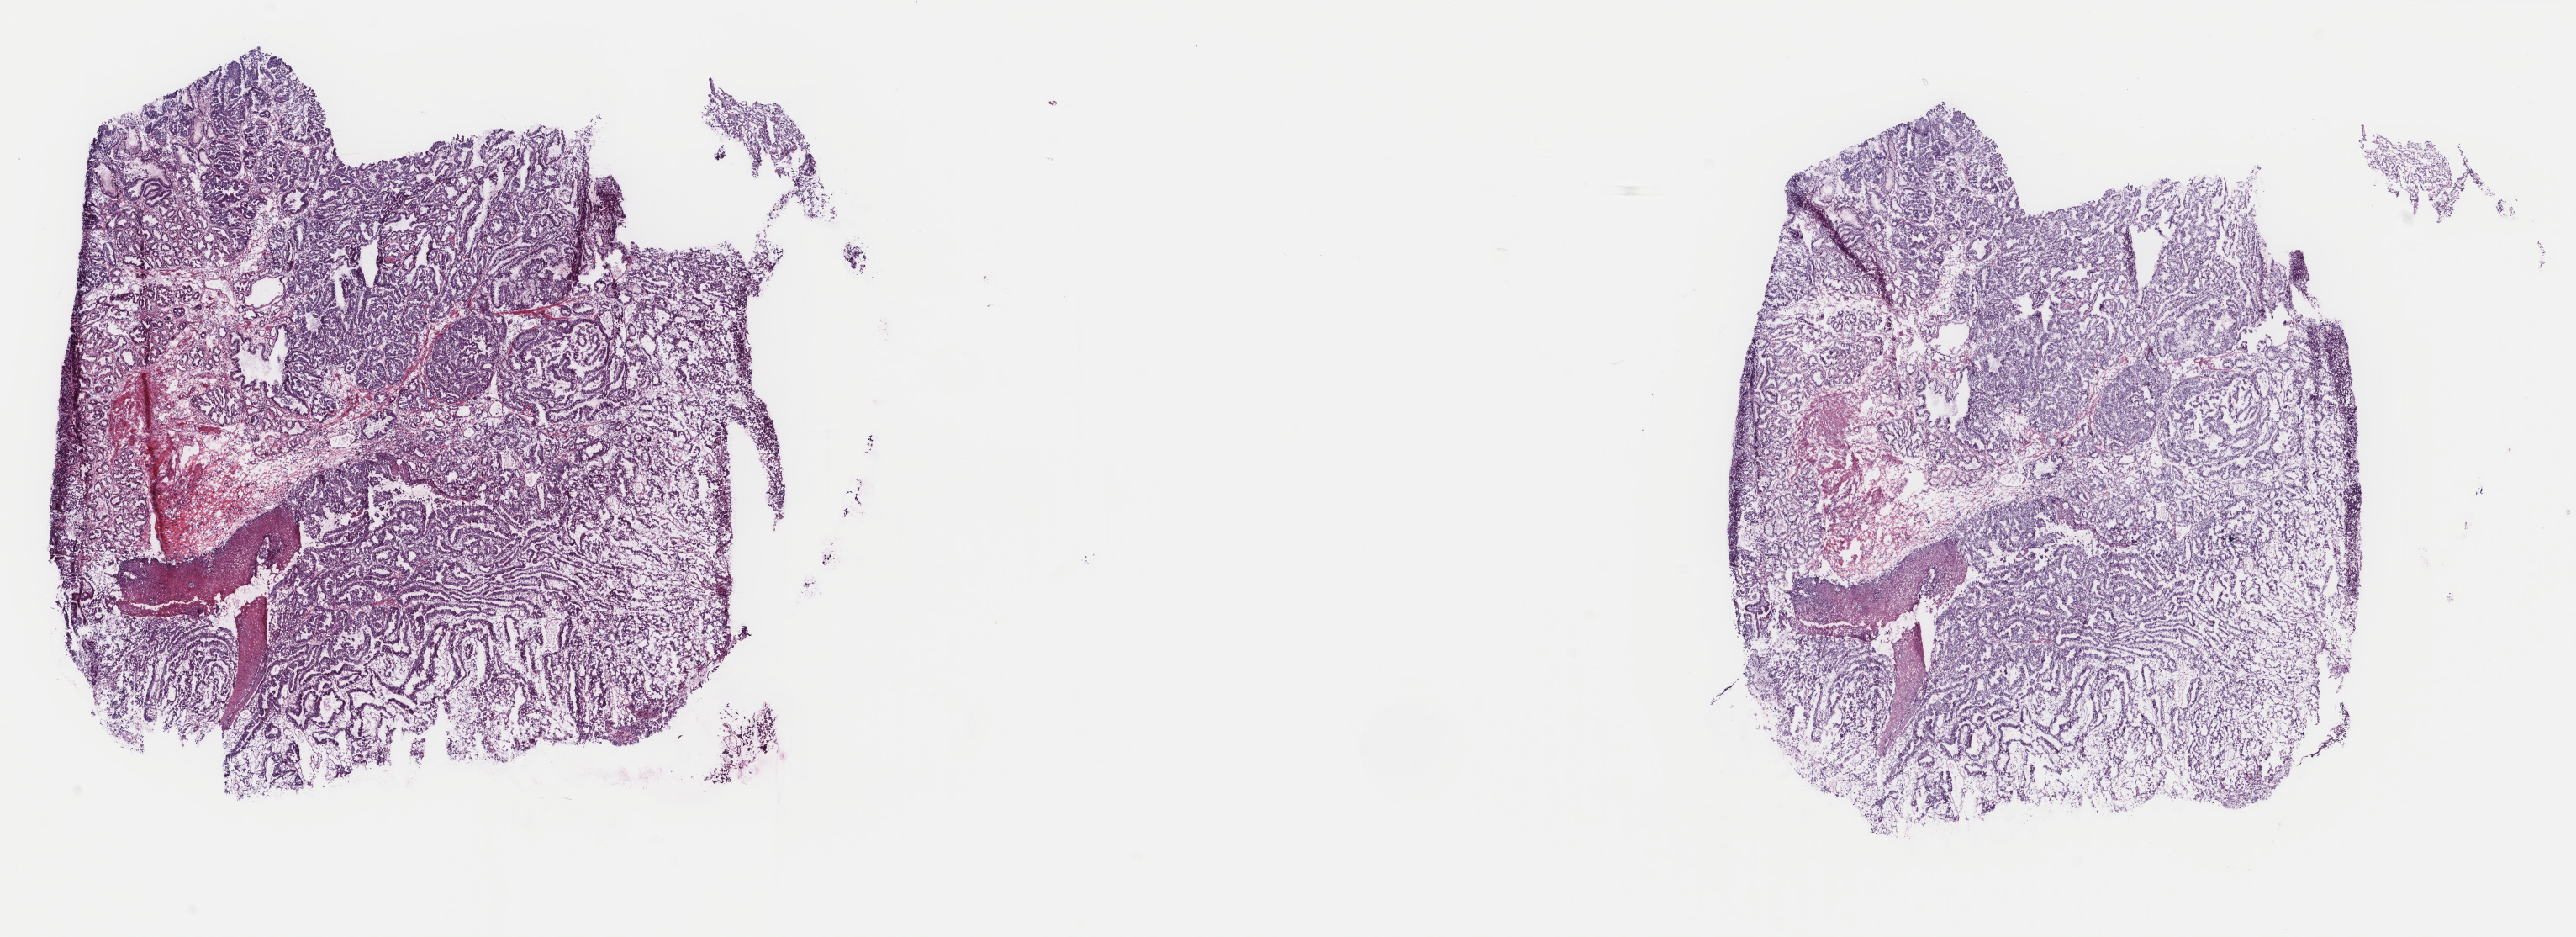
H&E-stained whole-slide image — whole scanned area (about 24.3 x 8.8 mm, acquisition: 40x scan) shown as a low-resolution overview, frozen section from the top of the tissue portion, sample: primary tumour, stomach. Female patient; age at initial diagnosis 72 years. Histologic grade: G2 (moderately differentiated). Slide review estimates, as recorded: tumour cells 95%, tumour nuclei 75%, normal cells 5%, stromal cells 0%, necrosis 0%. Inflammatory infiltration, as recorded: lymphocyte infiltration 5%, monocyte infiltration 0%, neutrophil infiltration 0%.
Histologic diagnosis: Adenocarcinoma, NOS. Lymph nodes positive (case pathology): 9 of 30 examined. AJCC pathologic stage: IIA.